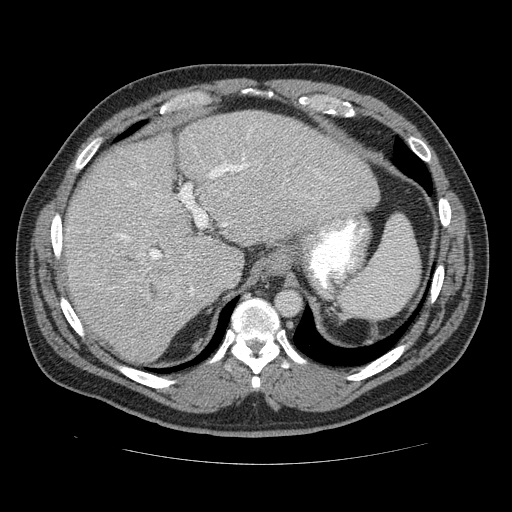
Contrast-enhanced abdominal CT (liver protocol), one axial slice. Reconstruction kernel STANDARD. 120 kVp. Soft-tissue window (W 400 / L 40 HU). 2.5 mm slice thickness. 512 × 512 image matrix, field of view 400 × 400 mm. Case-level facts recorded for this patient, not image findings: diagnosis: hepatocellular carcinoma (patient treated with transarterial chemoembolisation; whether this scan precedes or follows treatment is not stated here); TNM stage (as recorded): Stage-II; Child-Pugh class: B; tumour differentiation: moderately differentiated; tumour nodularity: multinodular.
Structures marked on this image (semi-automatically segmented with operator editing):
- liver parenchyma outside the tumour (the mass and vessels are separate outlines, so this box may not span the whole liver): bounding box [x1, y1, x2, y2] px = [56, 110, 380, 360]
- mass: [90, 243, 179, 309]
- liver vessels: [56, 154, 263, 295]